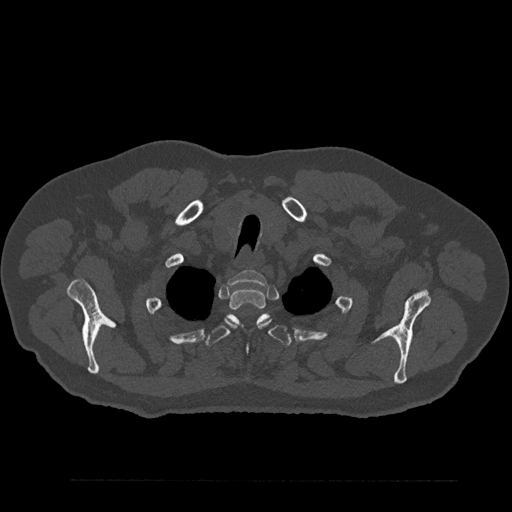
CT including the spine, one axial slice; position 708 of 797 along the scan axis; 120 kVp; bone window (W 1800 / L 400 HU); 0.5 mm slice thickness; 512 × 512 image matrix, field of view 430 × 430 mm. Male patient, age 61 years. Case-level facts recorded for this patient, not image findings: primary cancer: prostate.
Structures marked on this image (semi-automatic segmentation, software-assisted and operator-edited):
- T1 vertebra: bounding box (x1, y1, x2, y2) in pixels: (228, 270, 267, 285)
- T2 vertebra: (228, 288, 270, 328)
- T3 vertebra: (206, 313, 291, 379)